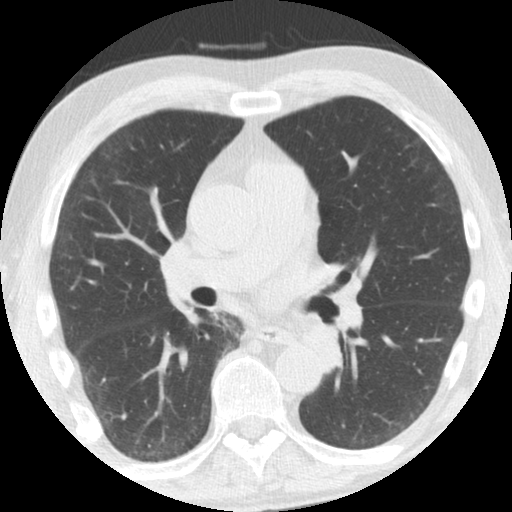
Low-dose screening chest CT, axial slice; third annual screen; lung window (W 1500 / L -600 HU); standard (soft-tissue) reconstruction kernel (STANDARD); 120 kVp. Male, age 61 years at enrolment.
Lesion marked by an expert reader, bounding box <295,316,345,362> (left, top, right, bottom; pixels). Screening reader's record for this exam: no non-calcified nodule ≥4 mm recorded. Participant outcome: lung cancer diagnosed 363 days after this screen — squamous cell carcinoma, NOS, left upper lobe, left lower lobe, well differentiated (G1), stage IIB (AJCC 6th edition), 100 mm at pathology.